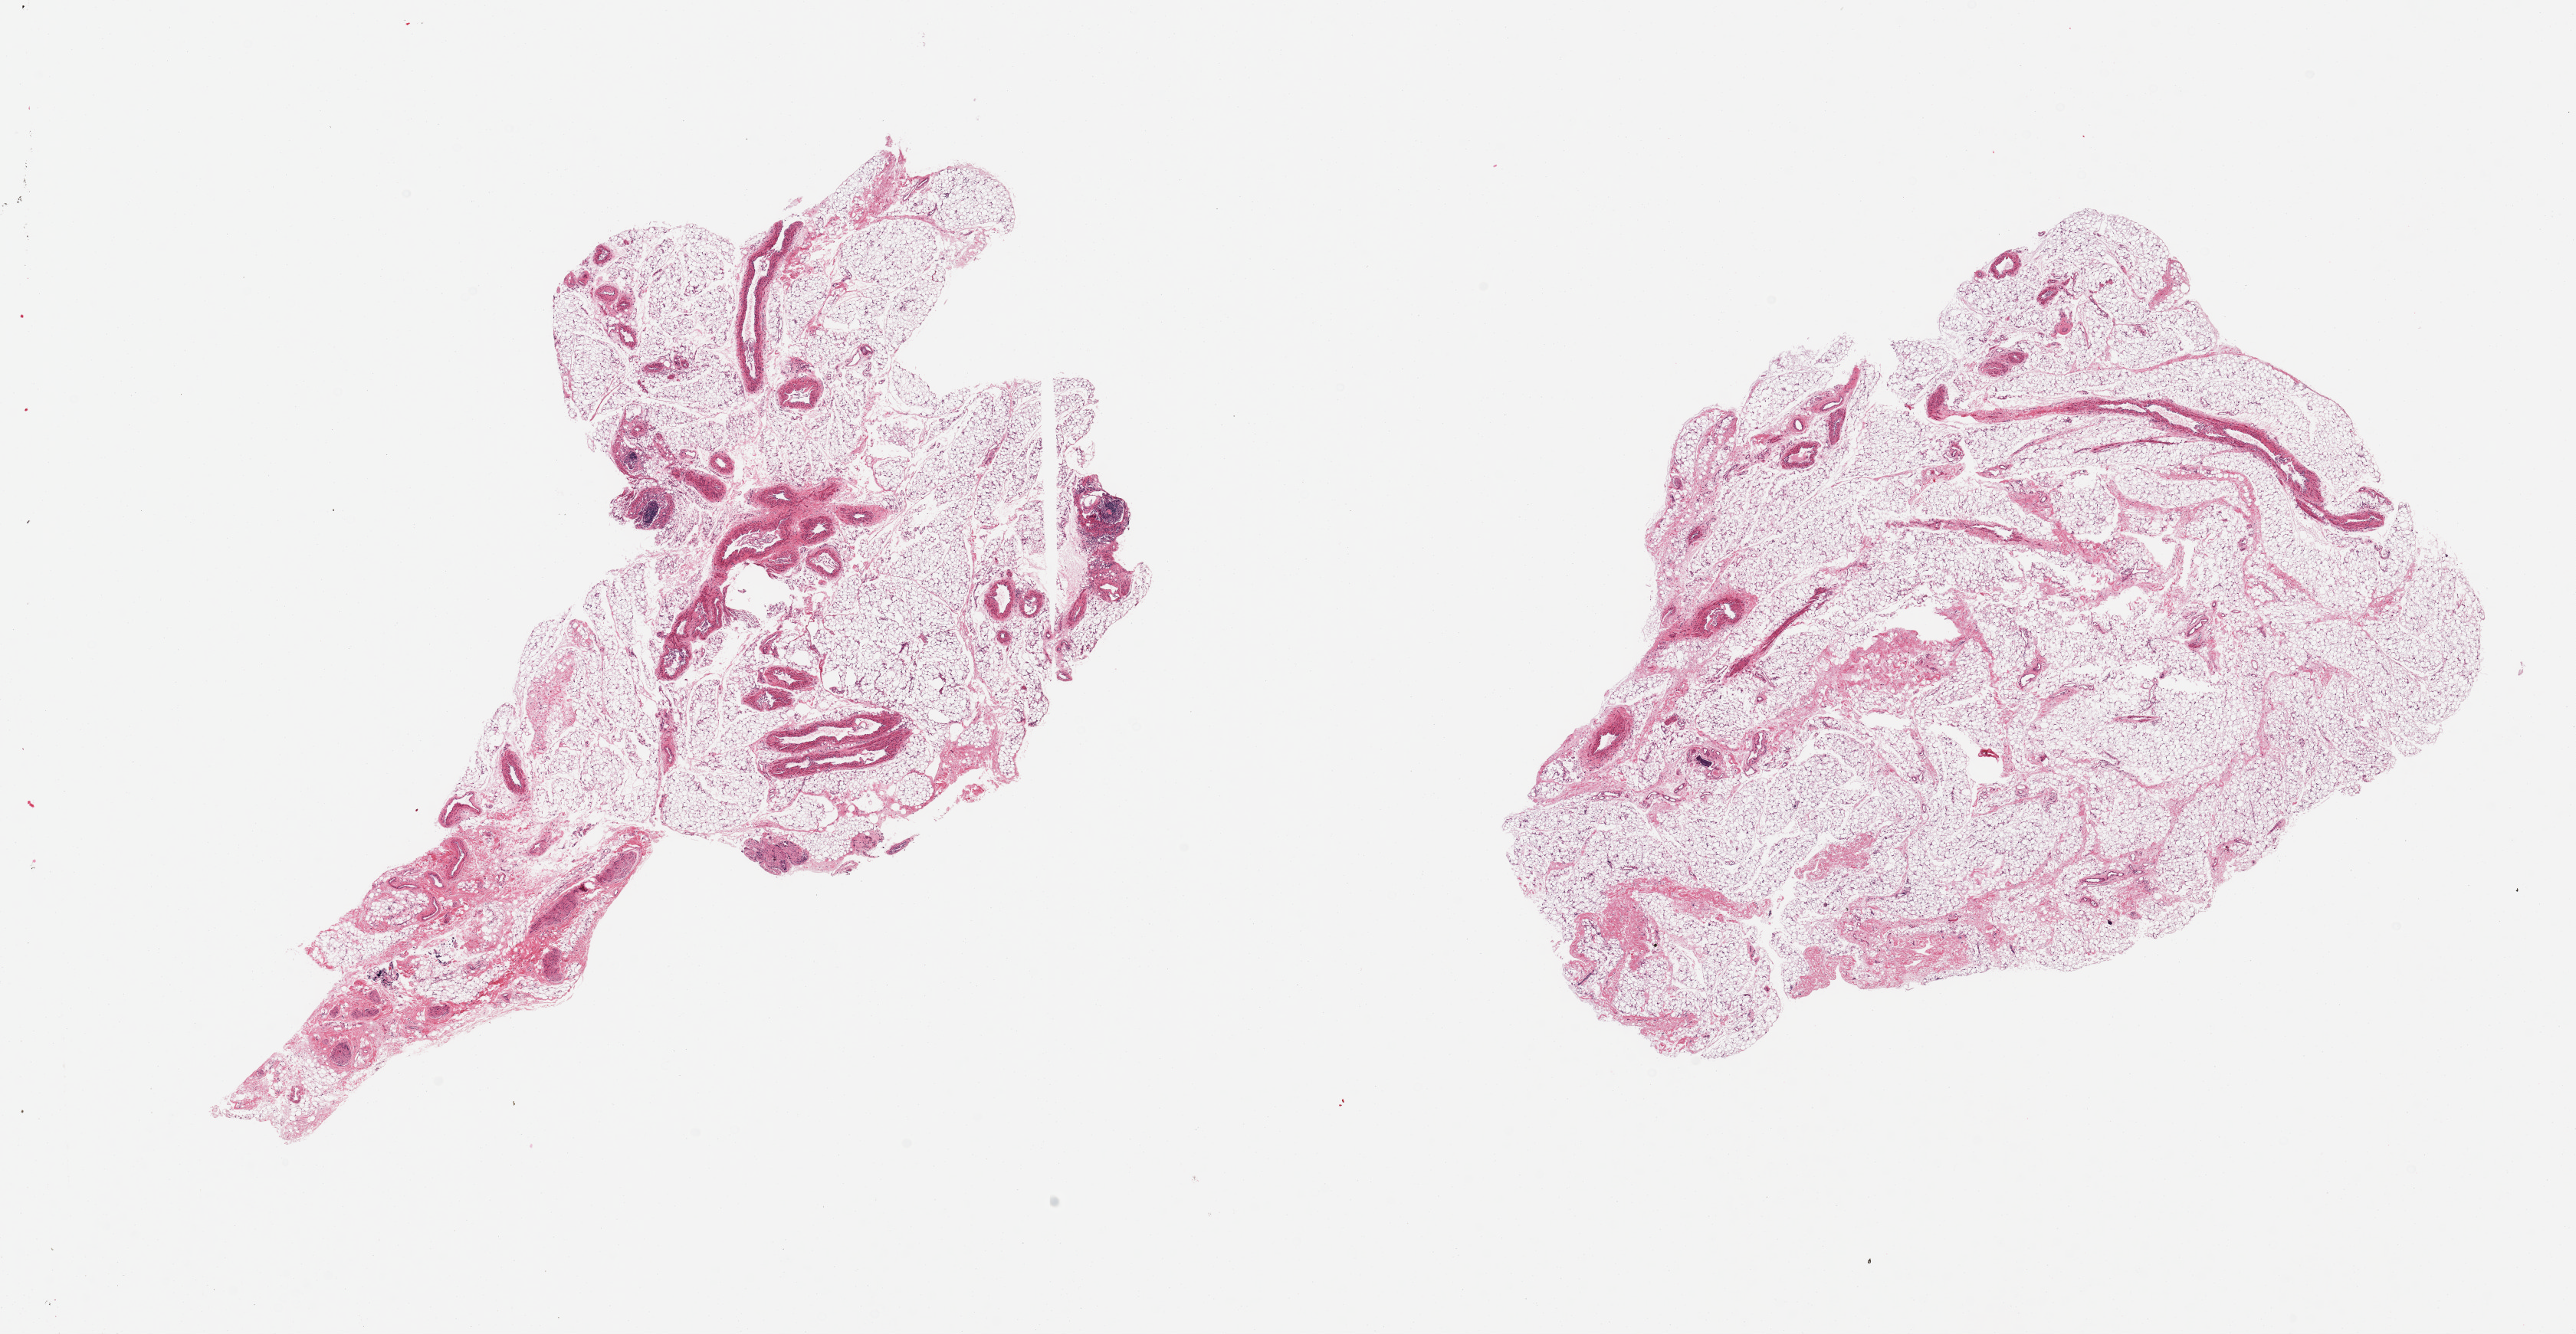
H&E whole-slide image, whole scanned area (about 26.6 x 13.8 mm, acquisition: 20x scan) shown as a low-resolution overview. PAXgene-fixed, paraffin-embedded tissue. Target tissue: omentum. Donor tissue sample. Donor sex: male.
Reviewer comment on this tissue sample: 2 pieces; 10% vascular content.